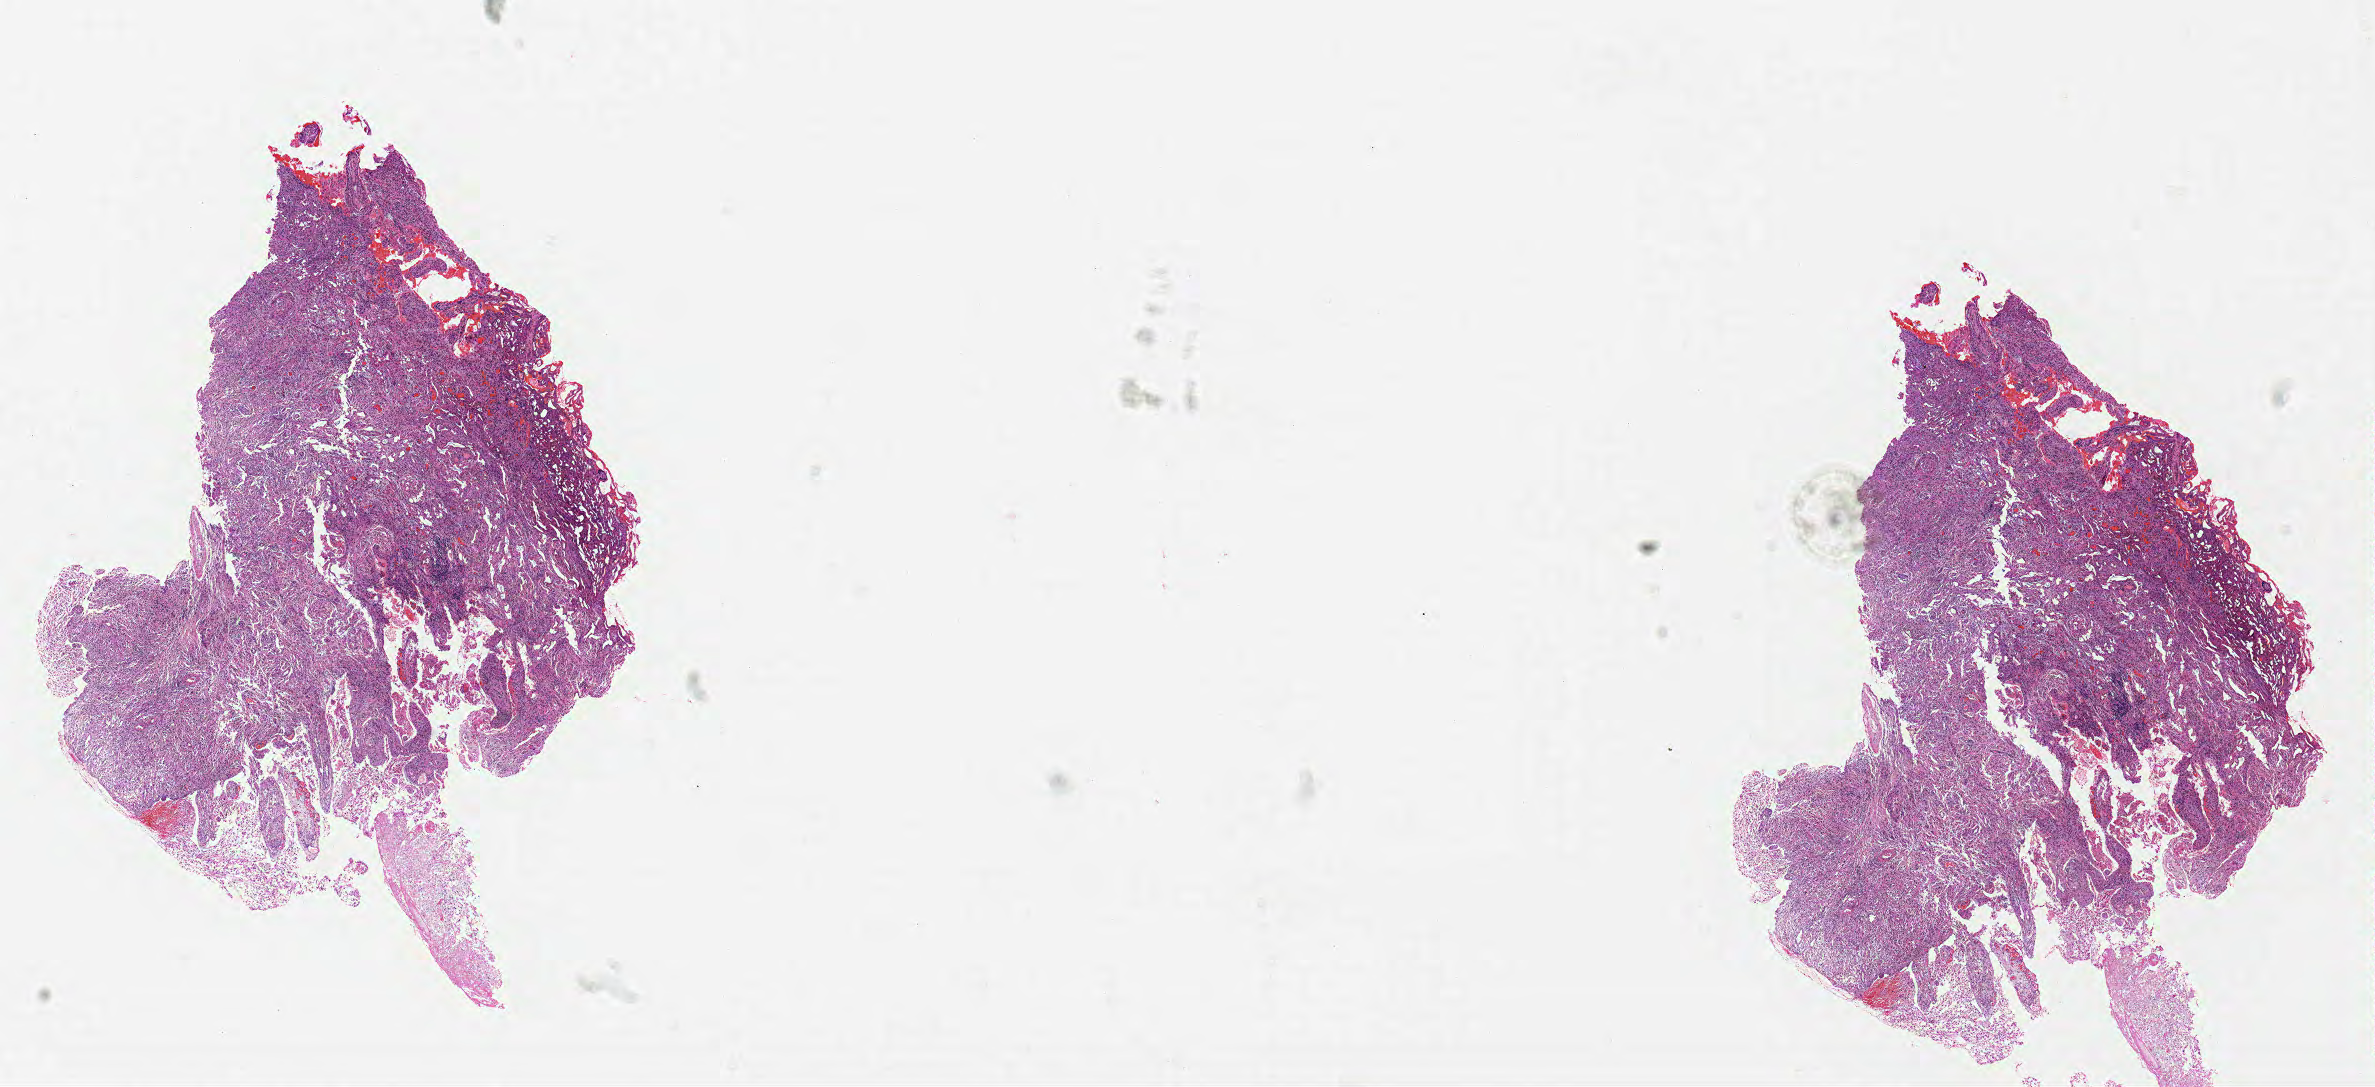
Whole-slide histology image, H&E, shown as a low-resolution overview of the whole scanned area (about 19.0 x 8.7 mm, from a 20x scan), FFPE section, brain, primary tumour sample. Female patient; age at initial diagnosis 48 years.
- pathologic diagnosis: Glioblastoma